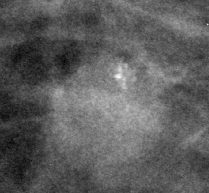
Cropped region of a digitized screen-film mammogram centred on a radiologist-marked abnormality; left breast; CC view.
- Finding: calcifications, morphology pleomorphic, distribution clustered; BI-RADS assessment category 4; subtlety rating 2 on a 1 (subtle) to 5 (obvious) scale; pathology result (as recorded, not read from the image): benign.